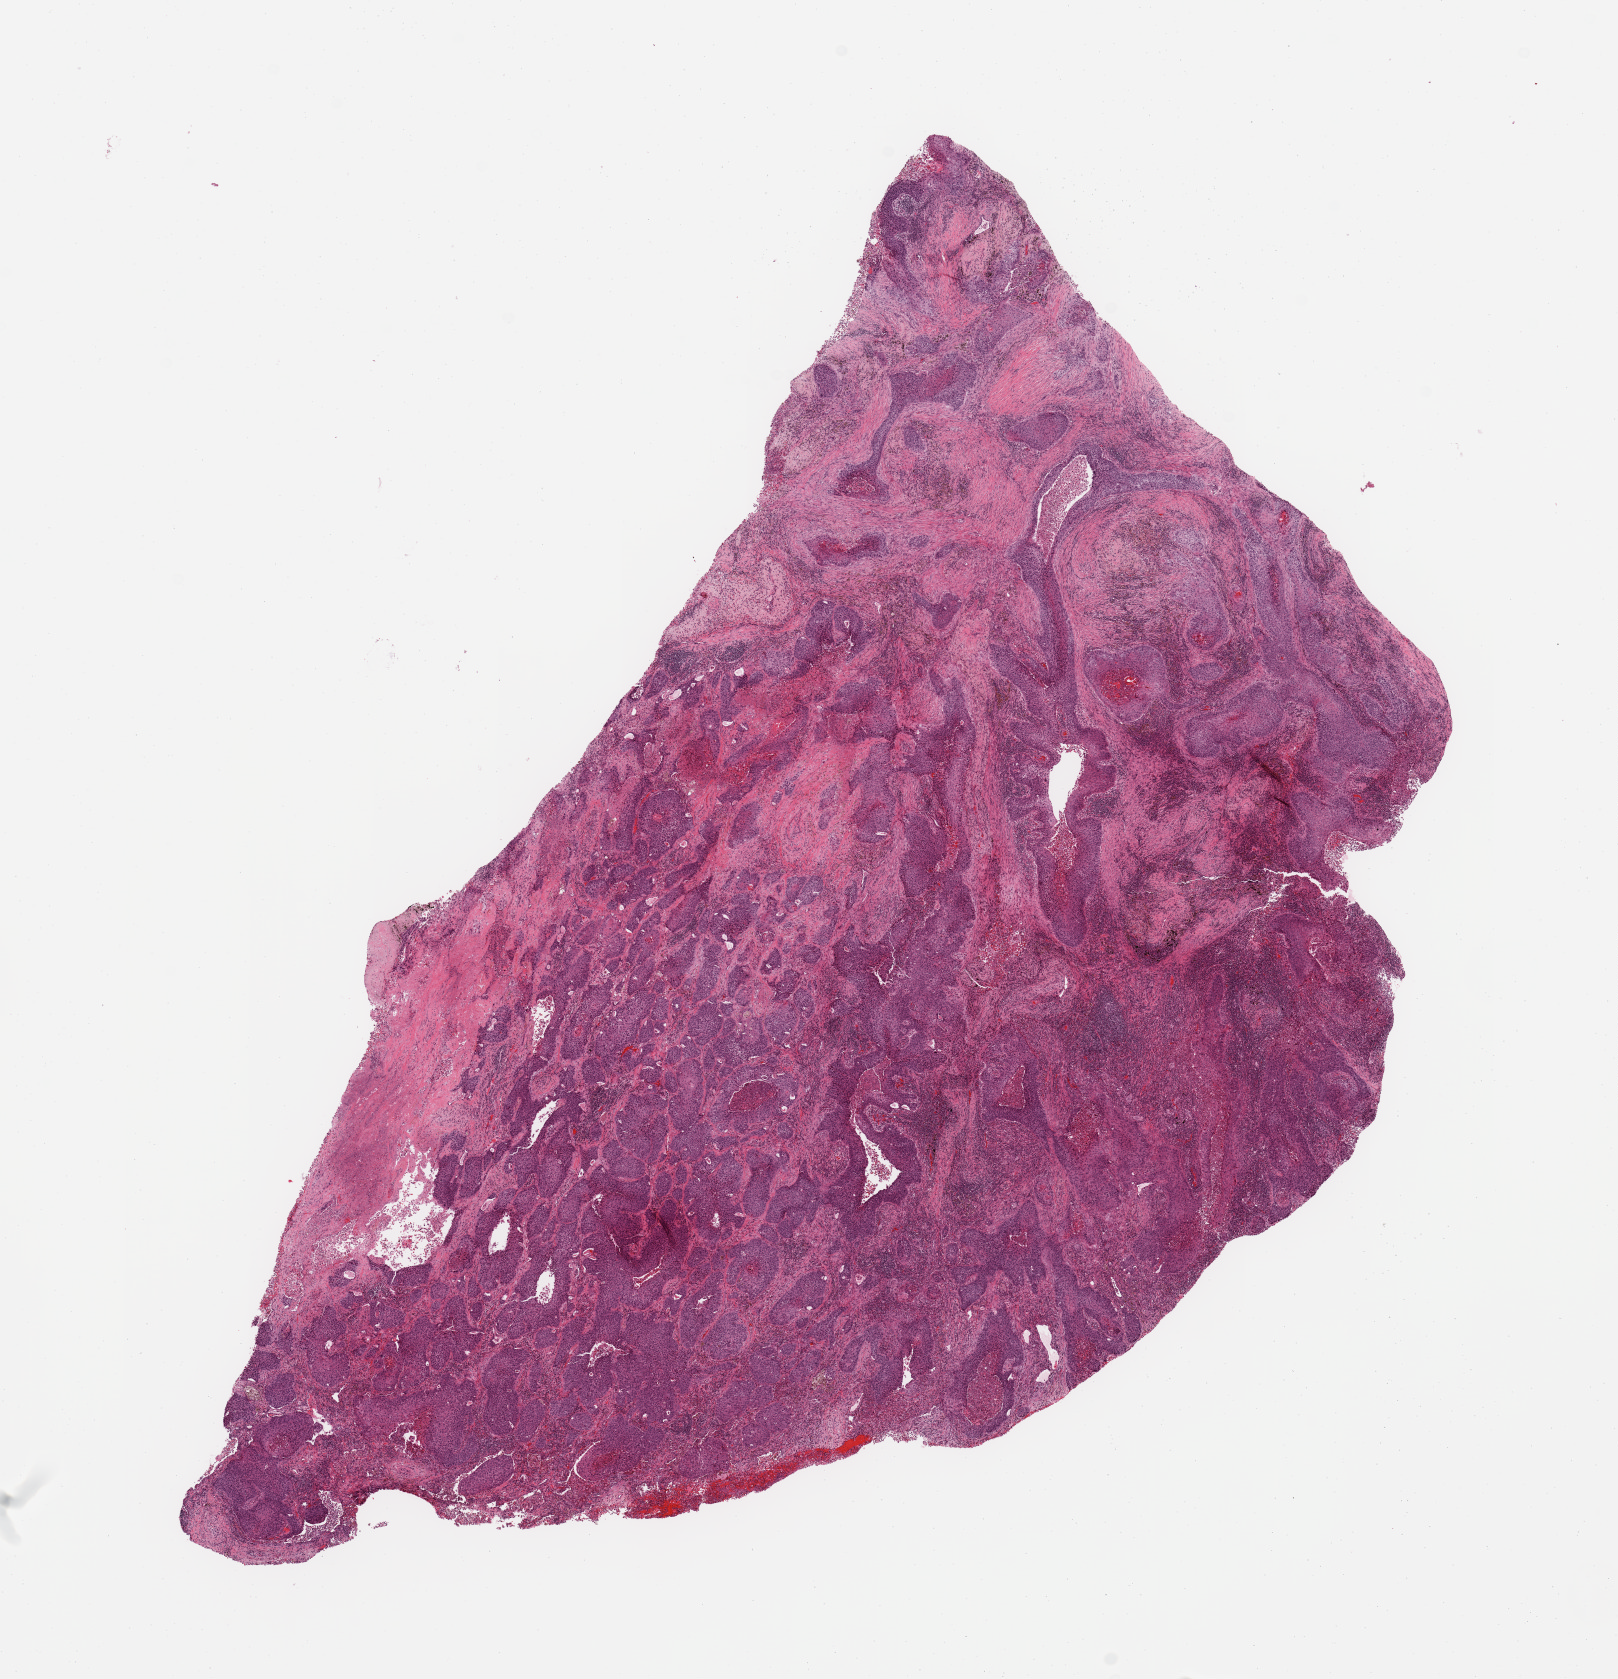
Hematoxylin and eosin (H&E) stained whole-slide image, whole scanned area (about 12.8 x 13.3 mm) shown as a low-resolution overview; tumour tissue sample, sampled site: lung. Patient: male, age 61 years. Slide review estimates, as recorded: tumour nuclei 70%, necrosis 8%.
Diagnosis: Squamous cell carcinoma, NOS.